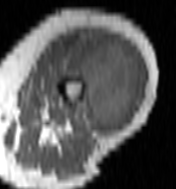
MRI of an extremity soft-tissue mass, one axial slice. Slice 45 of 100 in the series (ordered by position). MR volume resampled by the dataset authors to the PET/CT grid (not the native acquisition matrix). 3.27 mm slice thickness. 176 × 189 image matrix. Female patient. Case-level facts recorded for this patient, not image findings: histological type: undifferentiated – high grade; grade: high; site of the primary tumour: left thigh.
Structures marked on this image (expert contour drawn on MRI and transferred to this co-registered scan by the dataset authors):
- gross tumour volume including surrounding oedema: box from (x=55, y=34) to (x=141, y=133) px
- gross tumour volume (mass): (x=64, y=39)–(x=140, y=133)